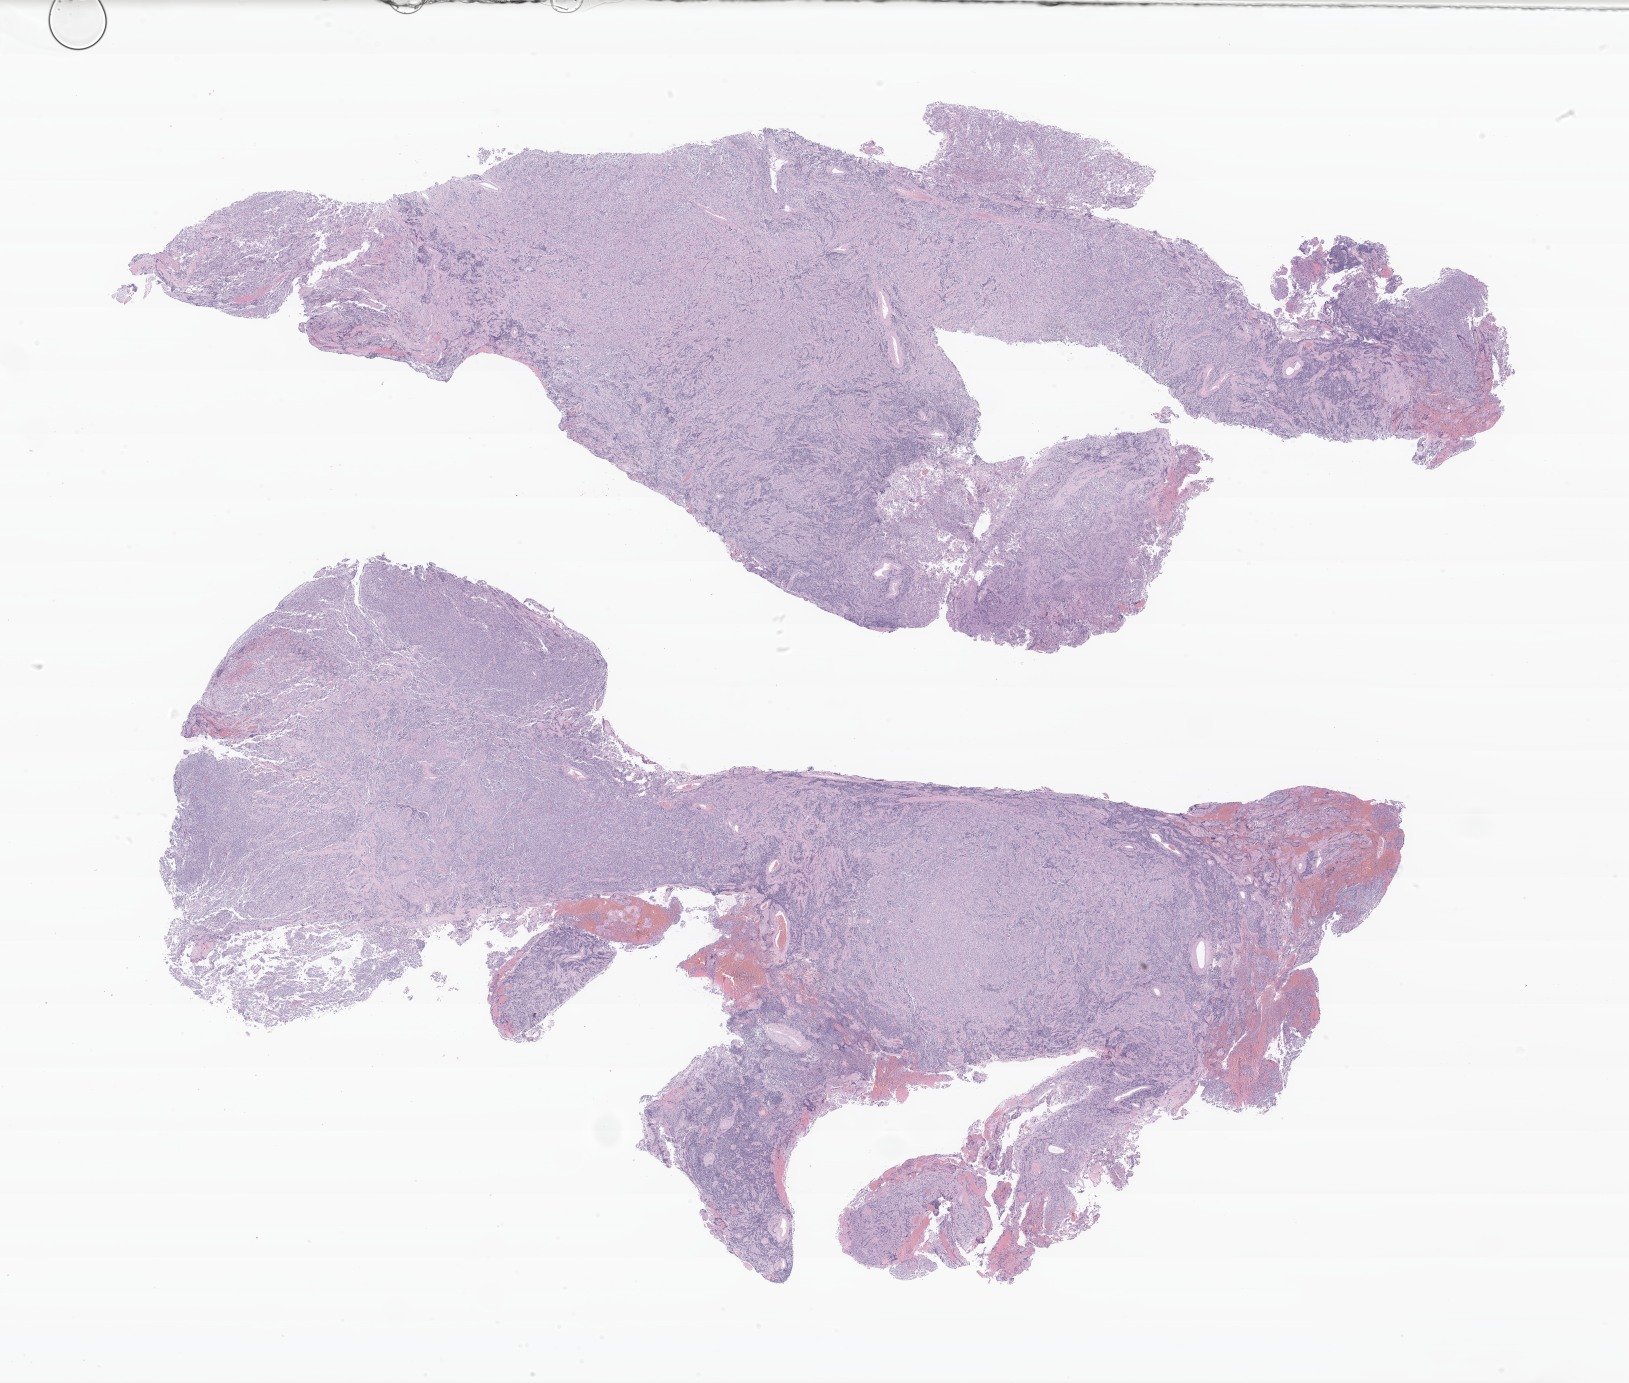
Digitized haematoxylin and eosin-stained section of tumor tissue from the cerebral ventricle — whole scanned area (about 27.4 x 23.3 mm) shown as a low-resolution overview. Formalin-fixed paraffin-embedded section. Patient male; age 113 months (9 years 5 months).
* diagnosis (ICD-O-3 morphology term): Medulloblastoma, NOS